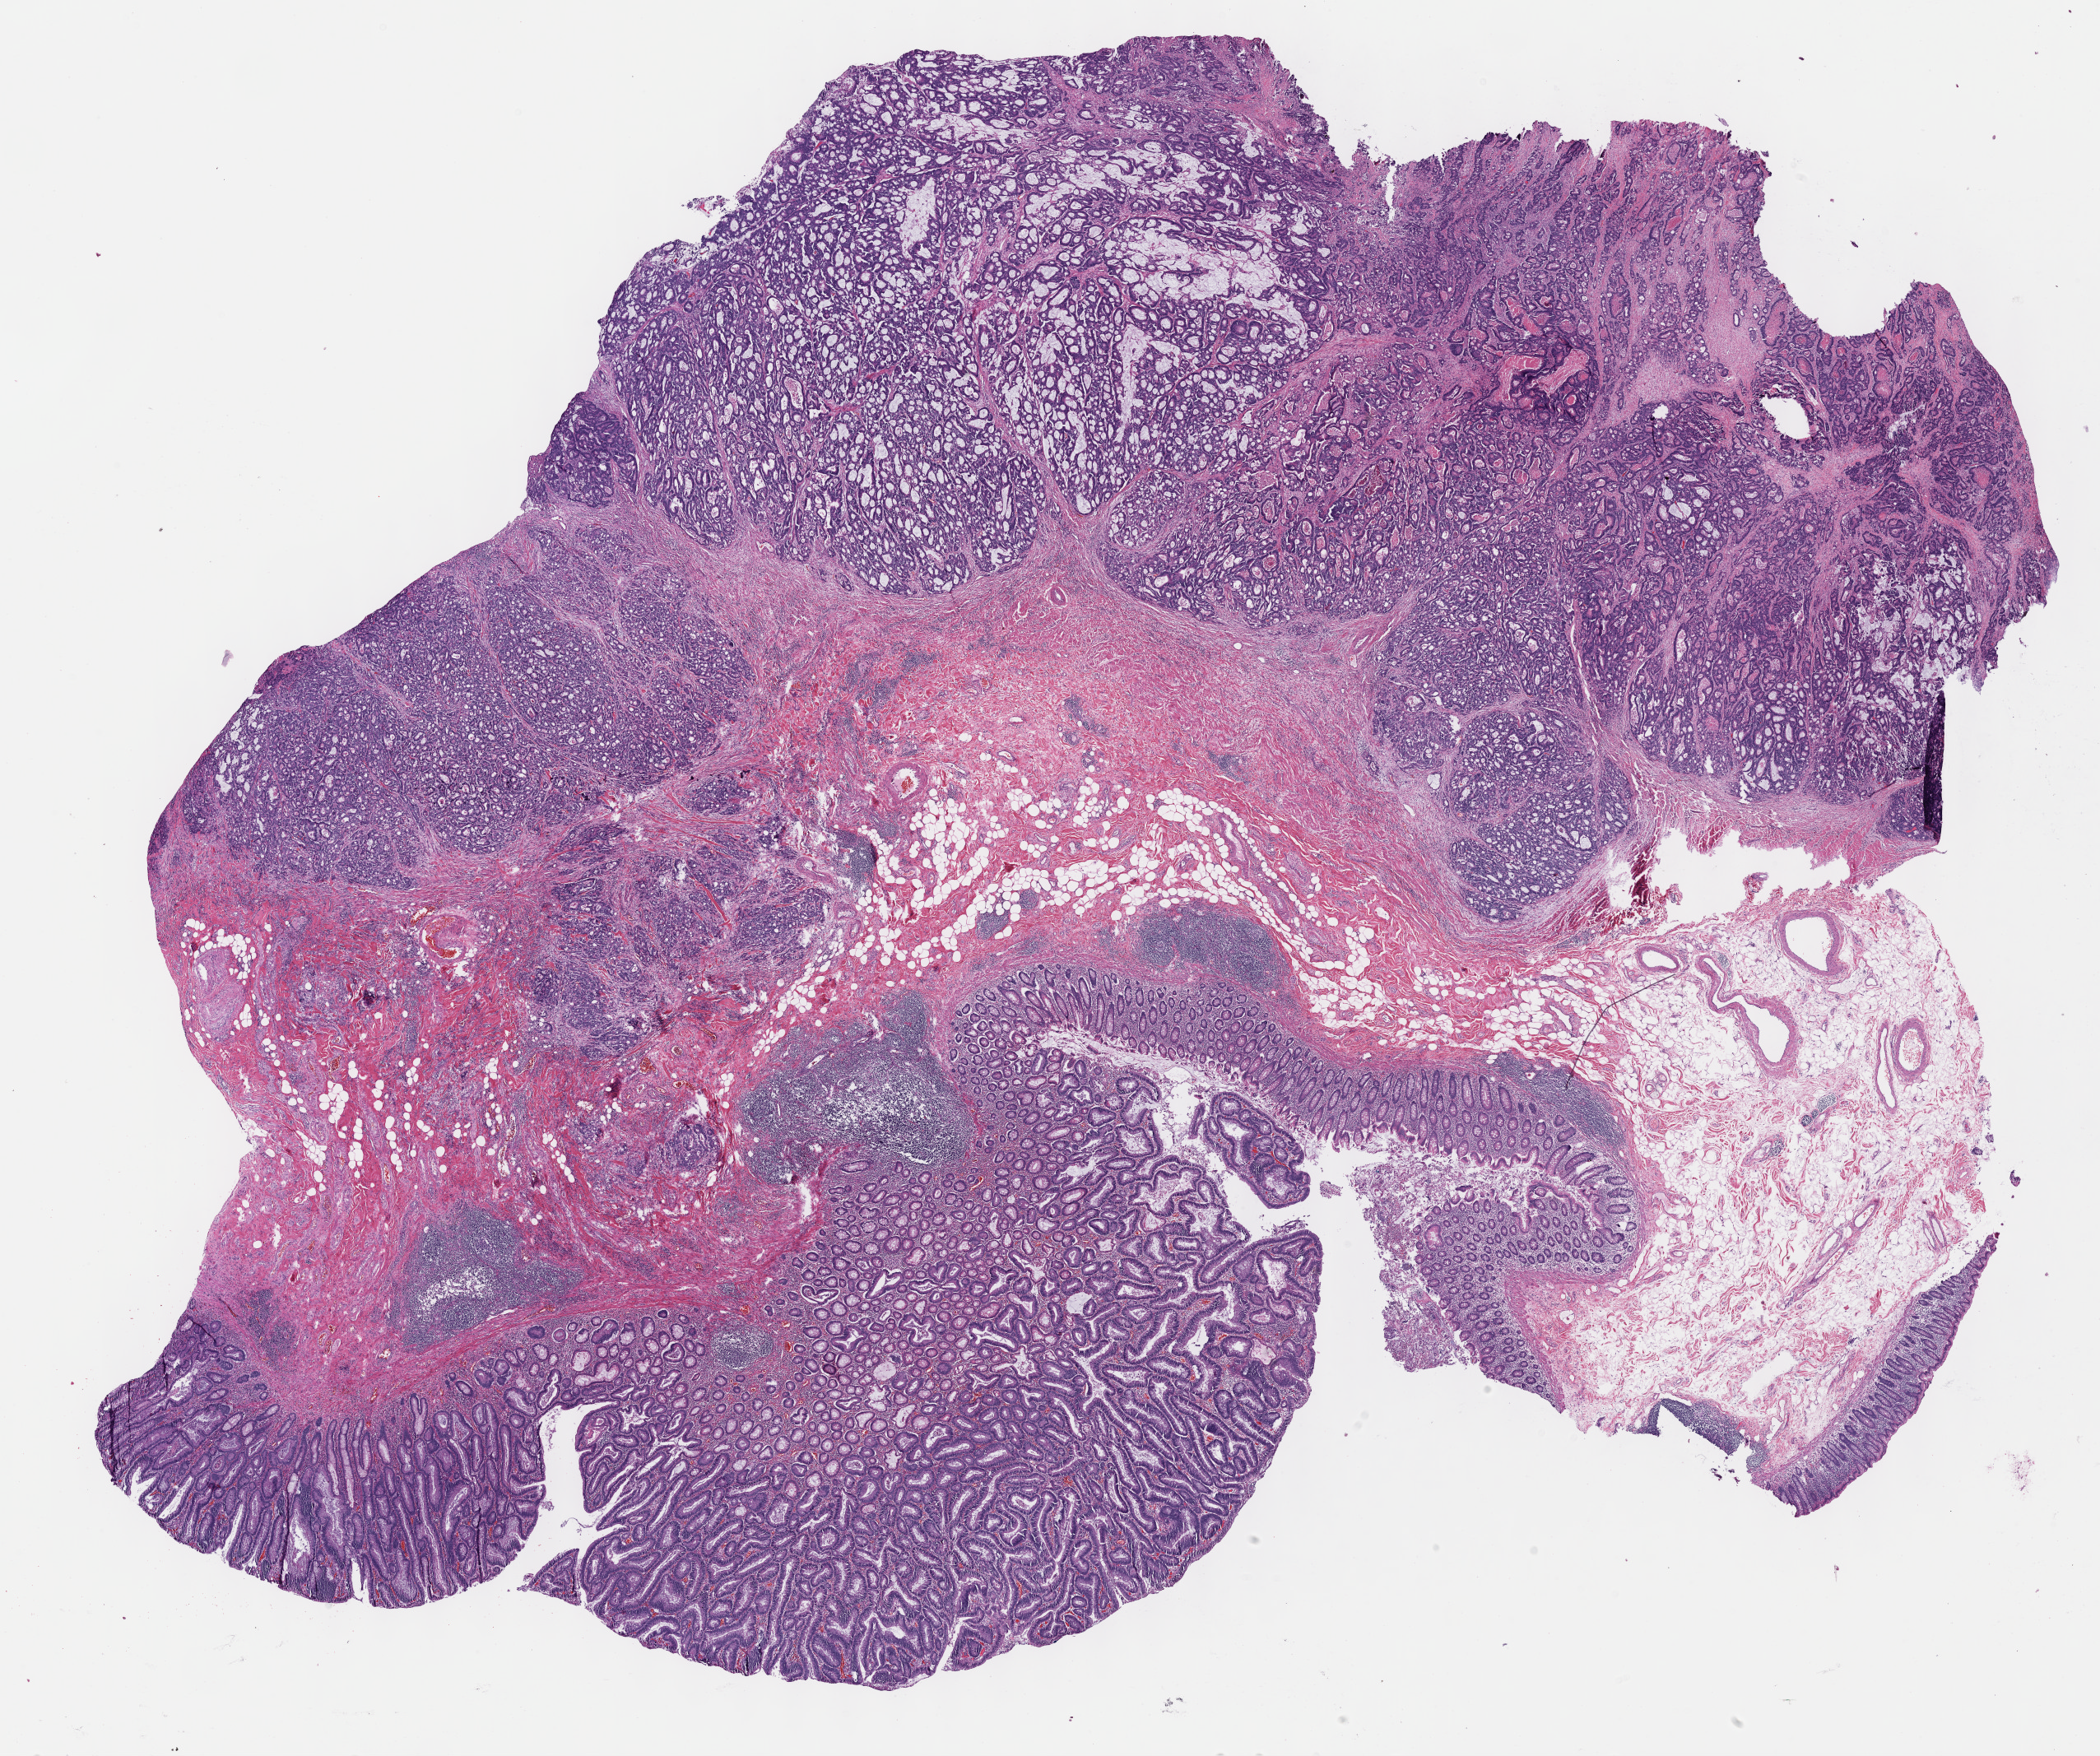
Digitized H&E tissue section (whole slide), shown as a low-resolution overview of the whole scanned area (about 20.6 x 17.3 mm, from a 40x scan). FFPE section. Colon, primary tumour sample. Male, age 42 years at initial diagnosis.
Histologic diagnosis: Mucinous adenocarcinoma. Lymph nodes positive (case pathology): 0 of 17 examined. AJCC pathologic stage: IVA.